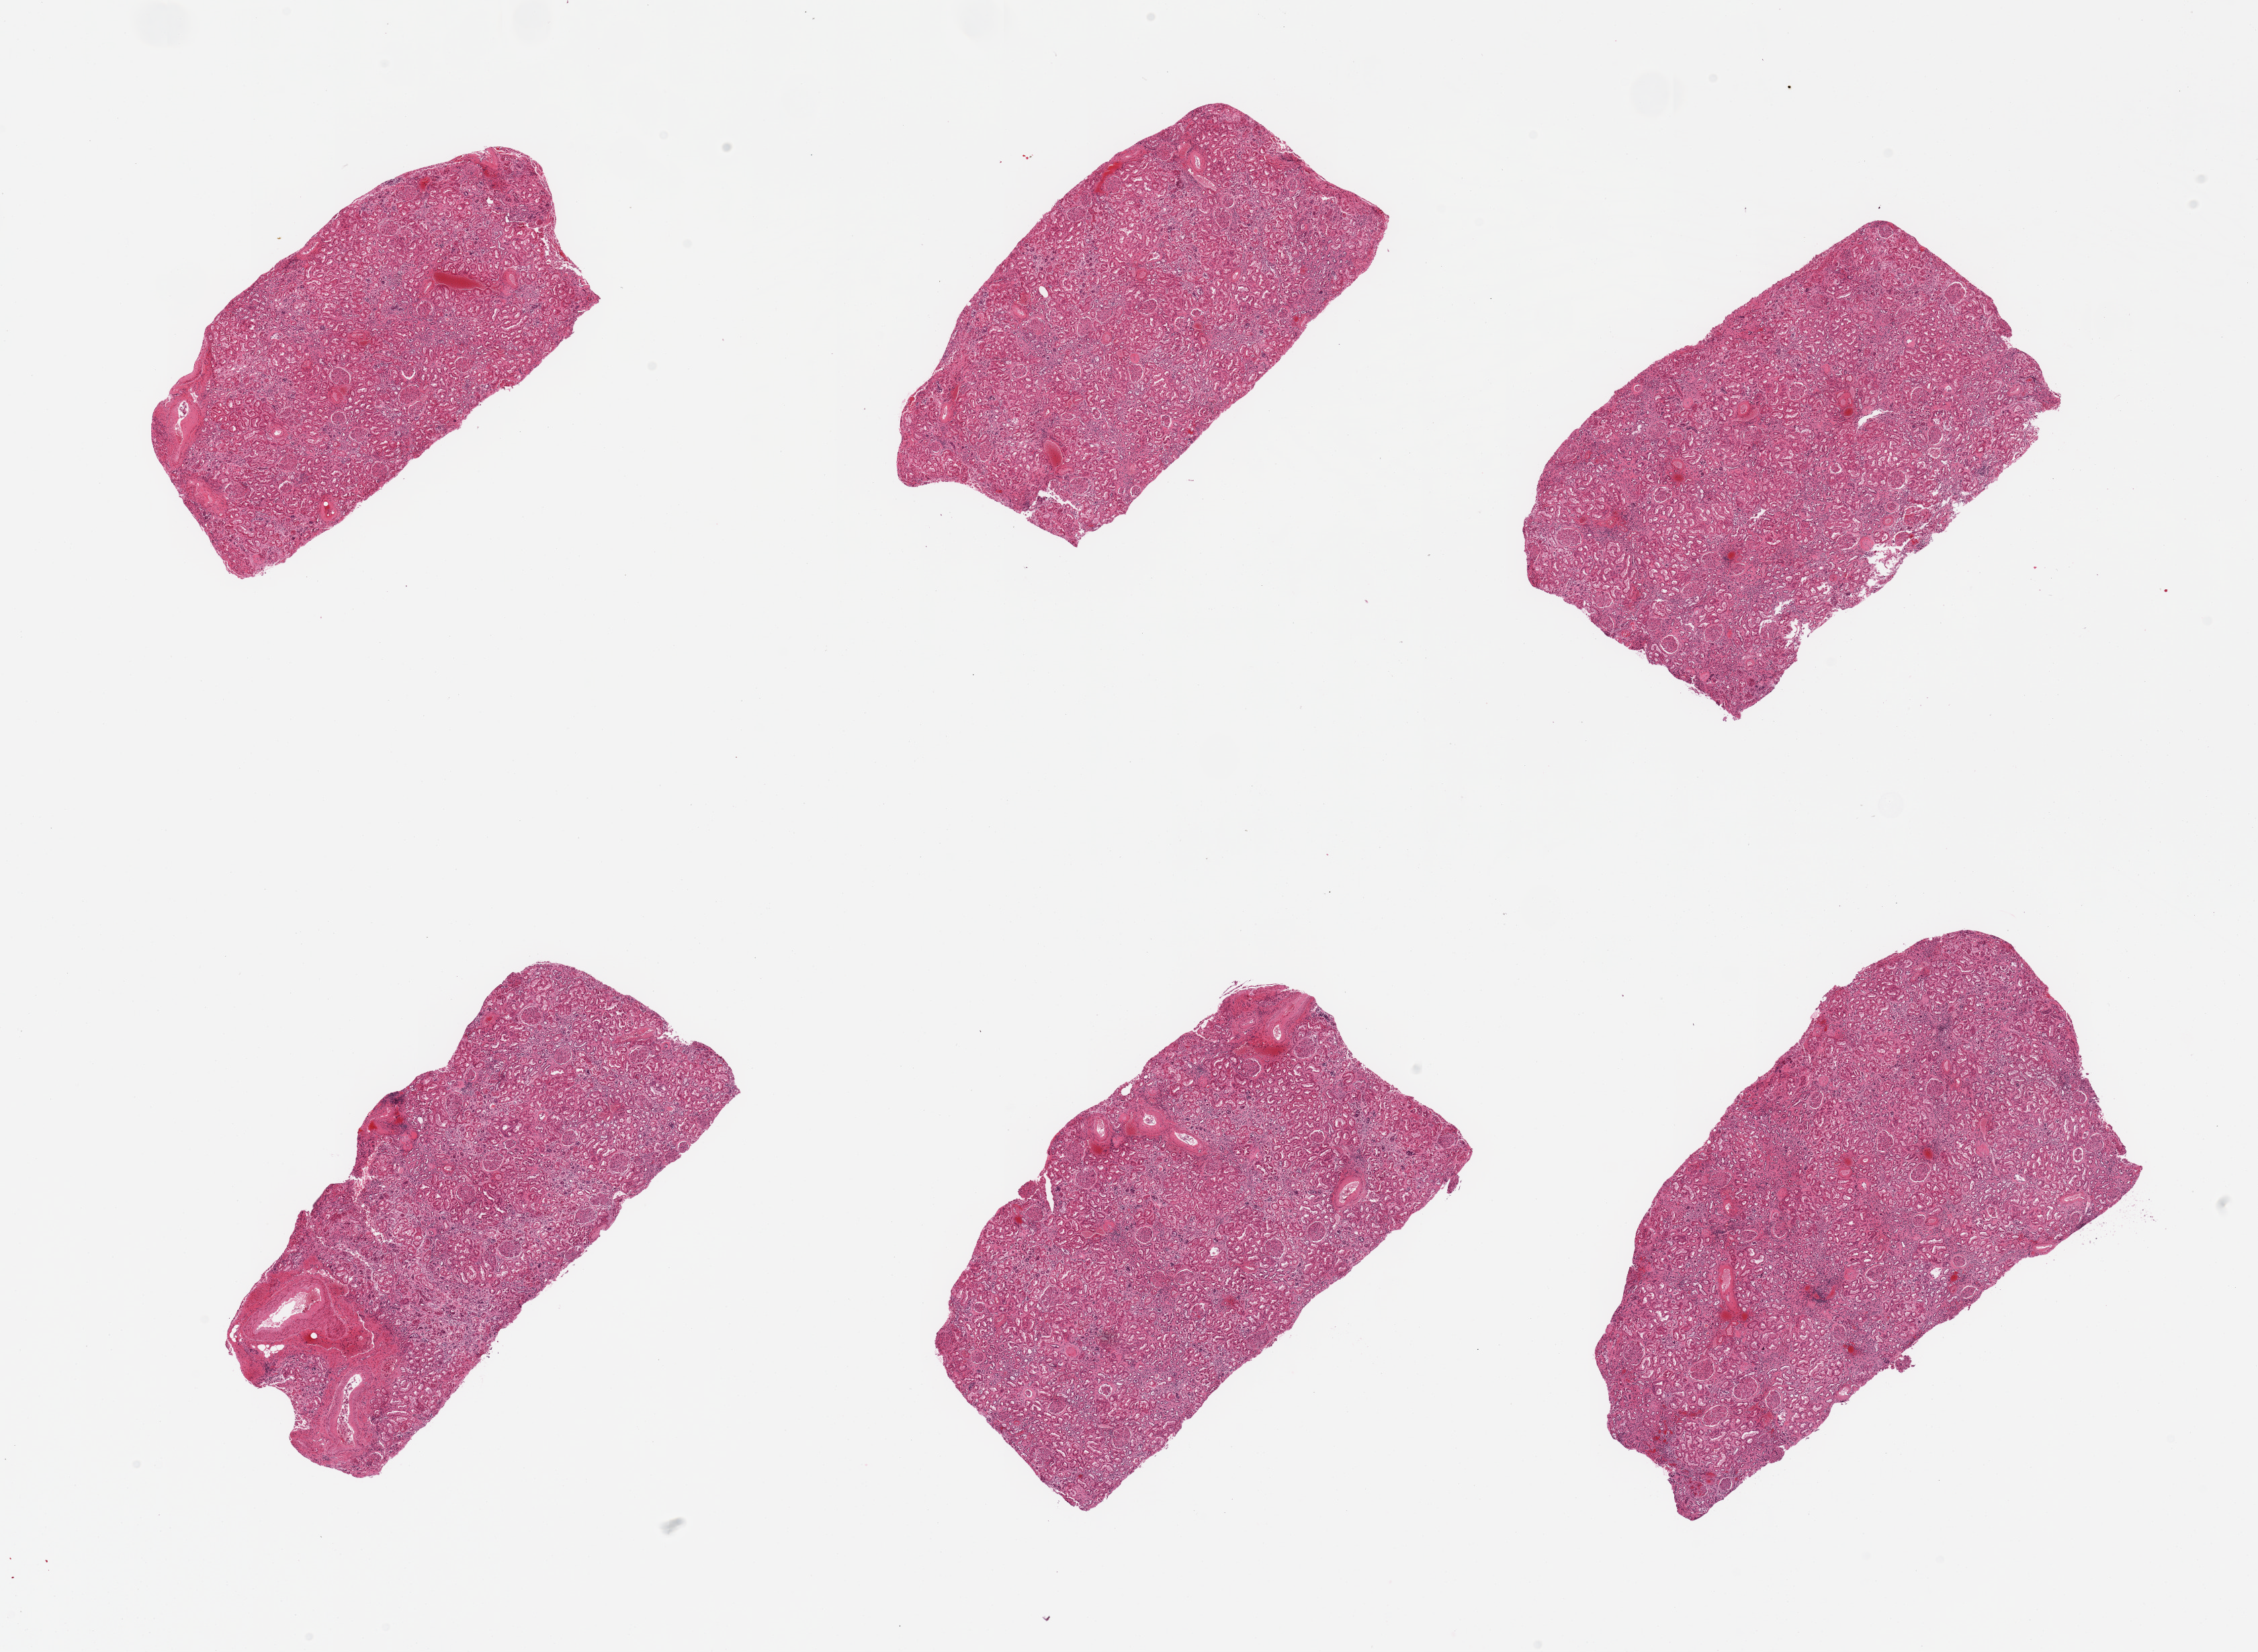
H&E whole-slide image, brightfield — low-resolution overview of the scanned area, about 26.6 x 19.4 mm, PAXgene-fixed, paraffin-embedded tissue, target tissue: renal cortex, tissue donor sample.
Review note (as recorded): 6 pieces, markedly autolzyed; glomeruli present.